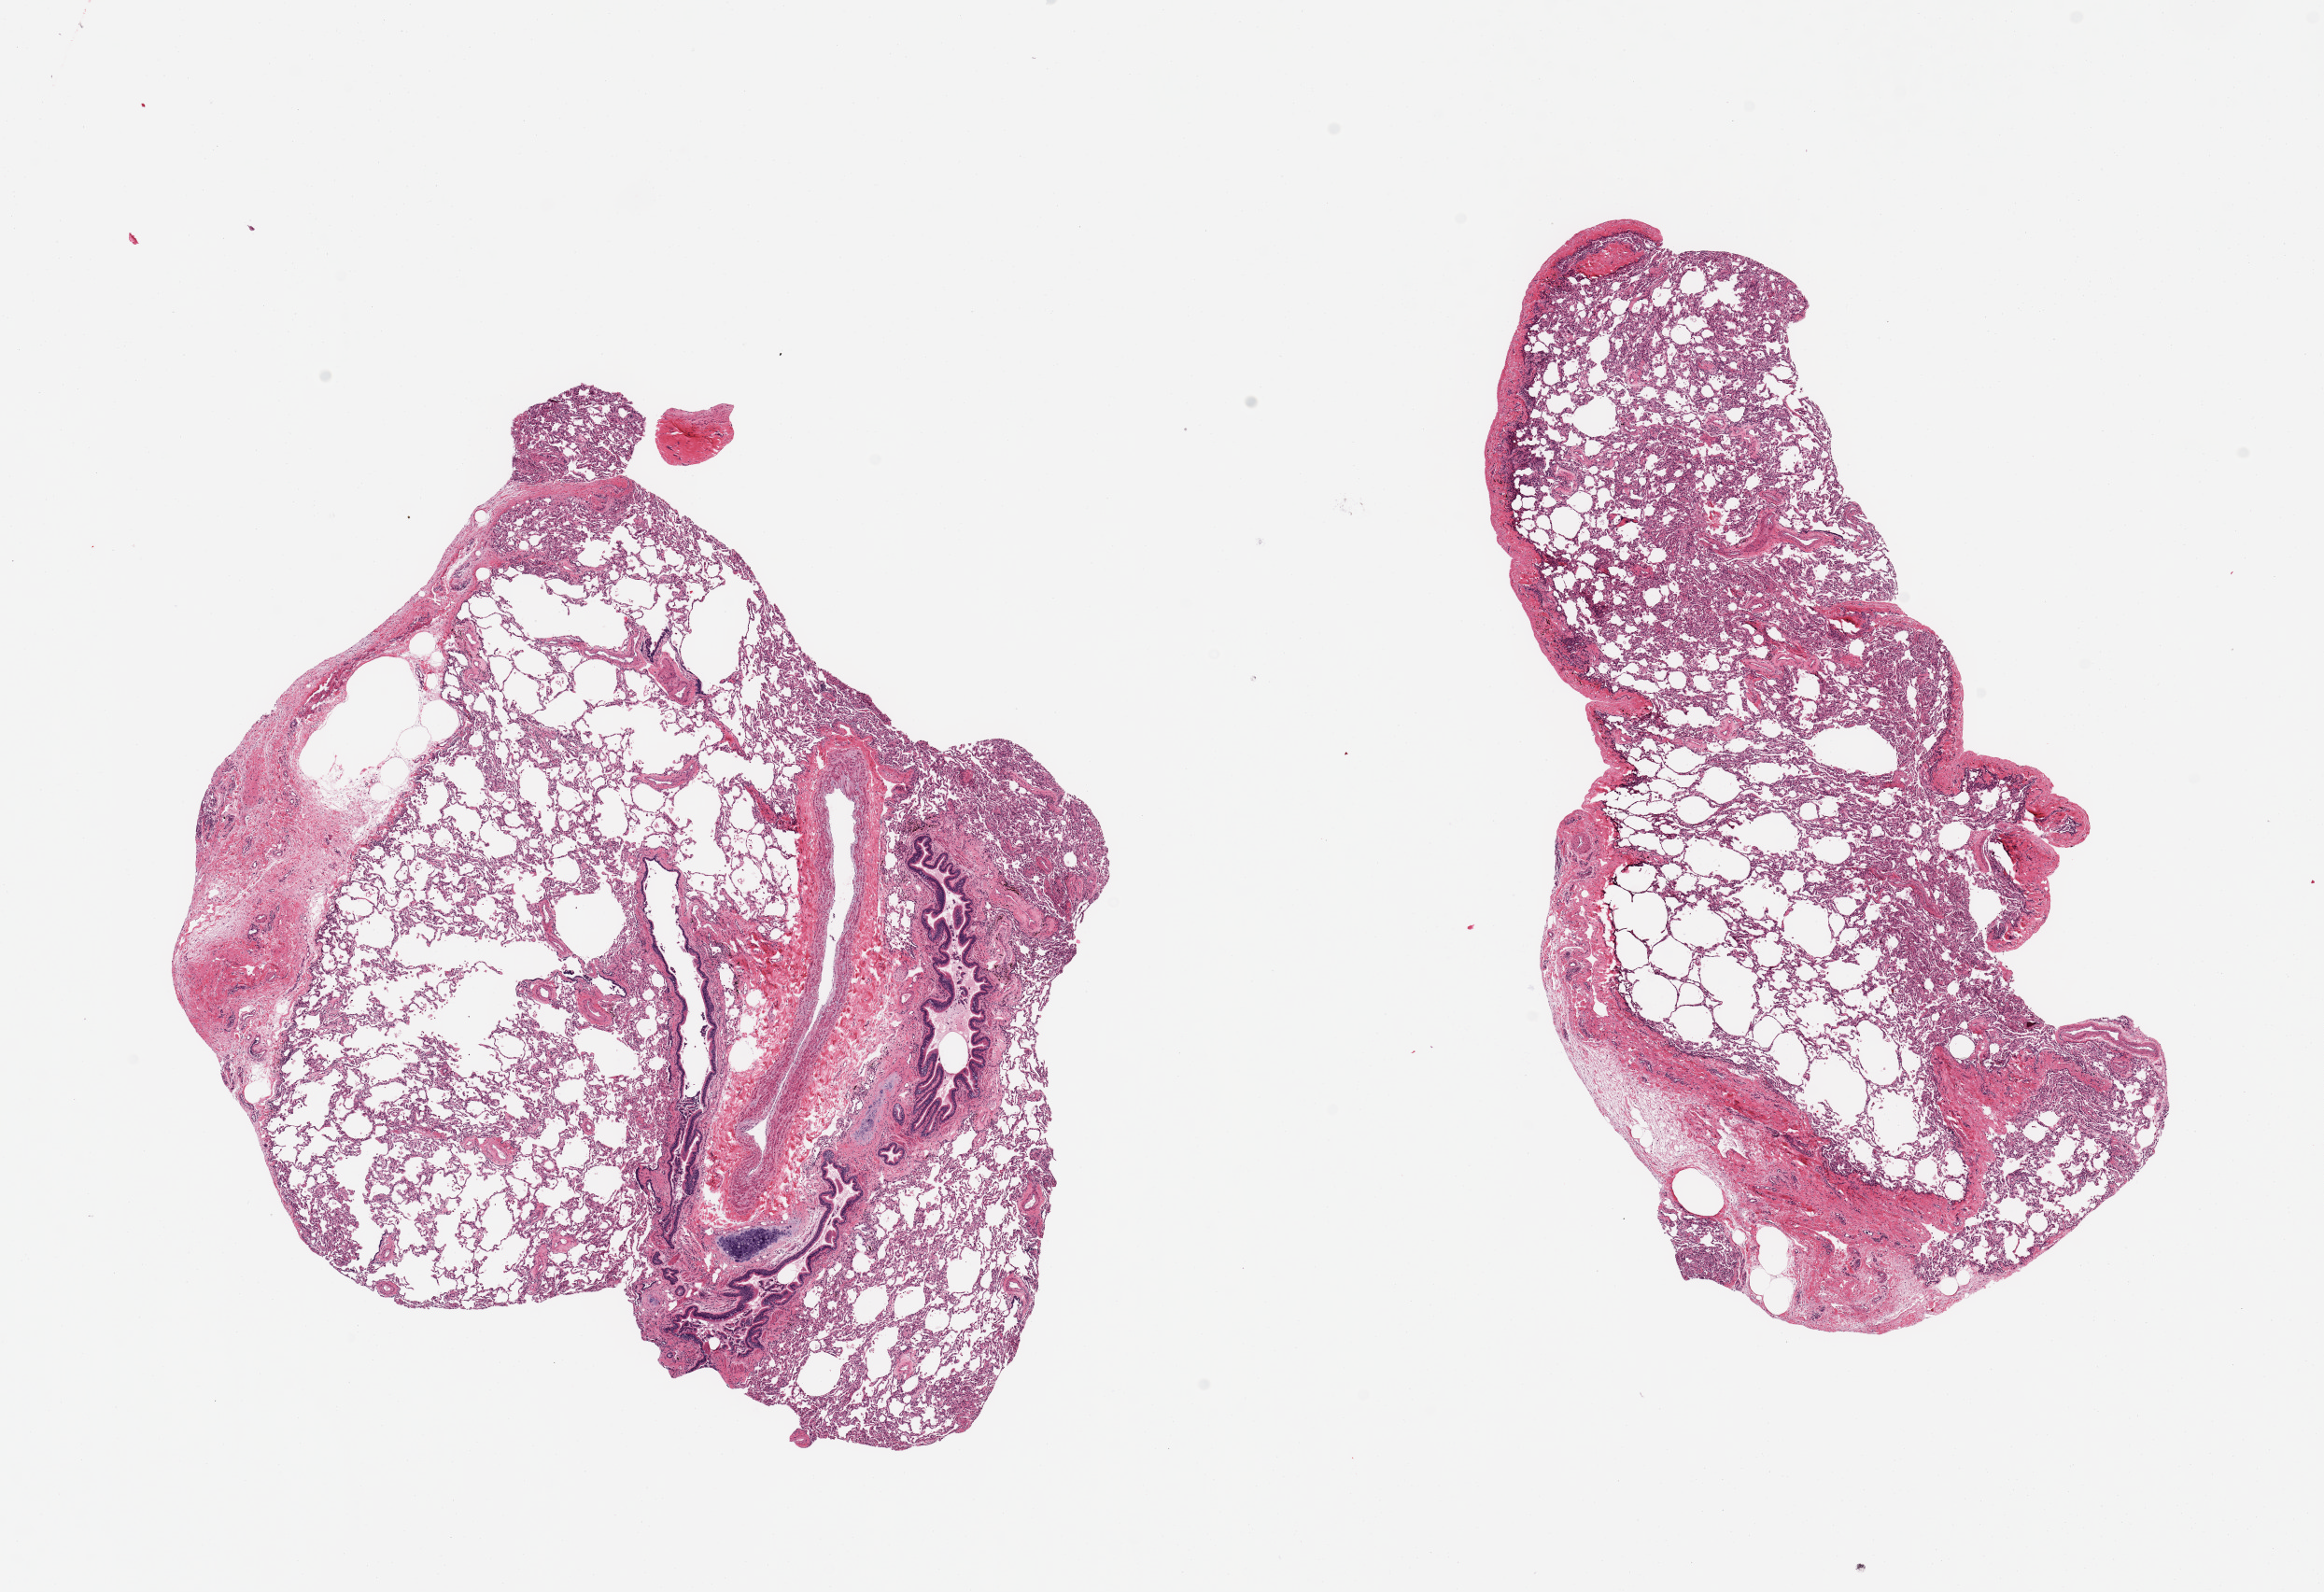
Digitized hematoxylin and eosin (H&E)-stained section, brightfield, whole scanned area (about 19.7 x 13.5 mm, acquisition: 20x scan) shown as a low-resolution overview; PAXgene-fixed, paraffin-embedded tissue; section of lung (target tissue); donor tissue sample. Donor: male.
* pathologist's review note for this sample: 2 pieces; emphysema; several large bronchi and vessels in one piece; prominent fibrous bands